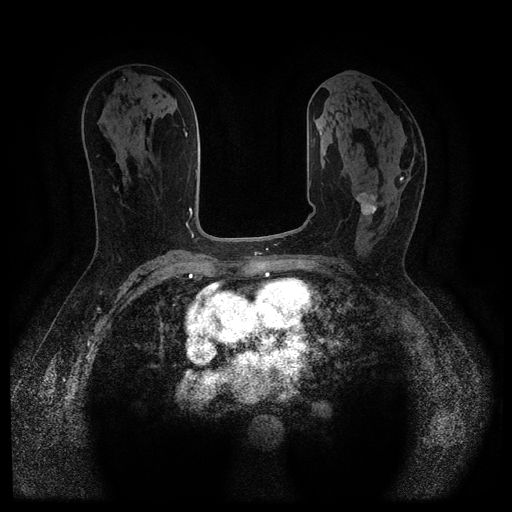
Breast MRI (dynamic contrast-enhanced, multi-phase), one axial slice; position 54 of 116 along the scan axis; dynamic contrast-enhanced series, time point 2 of 5 at this slice position (early post-contrast); 1.5 T; TE 2.6 ms, TR 5.4 ms; 2 mm slice thickness; 512 × 512 image matrix, field of view 340 × 340 mm. Female patient, age 64 years.
Structures marked on this image (semi-automatically segmented with operator editing):
- breast lesion (labelled 'tumour' in the annotation; benign lesions carry a separate 'benign' label): bounding box (x1, y1, x2, y2) in pixels: (356, 192, 384, 217)